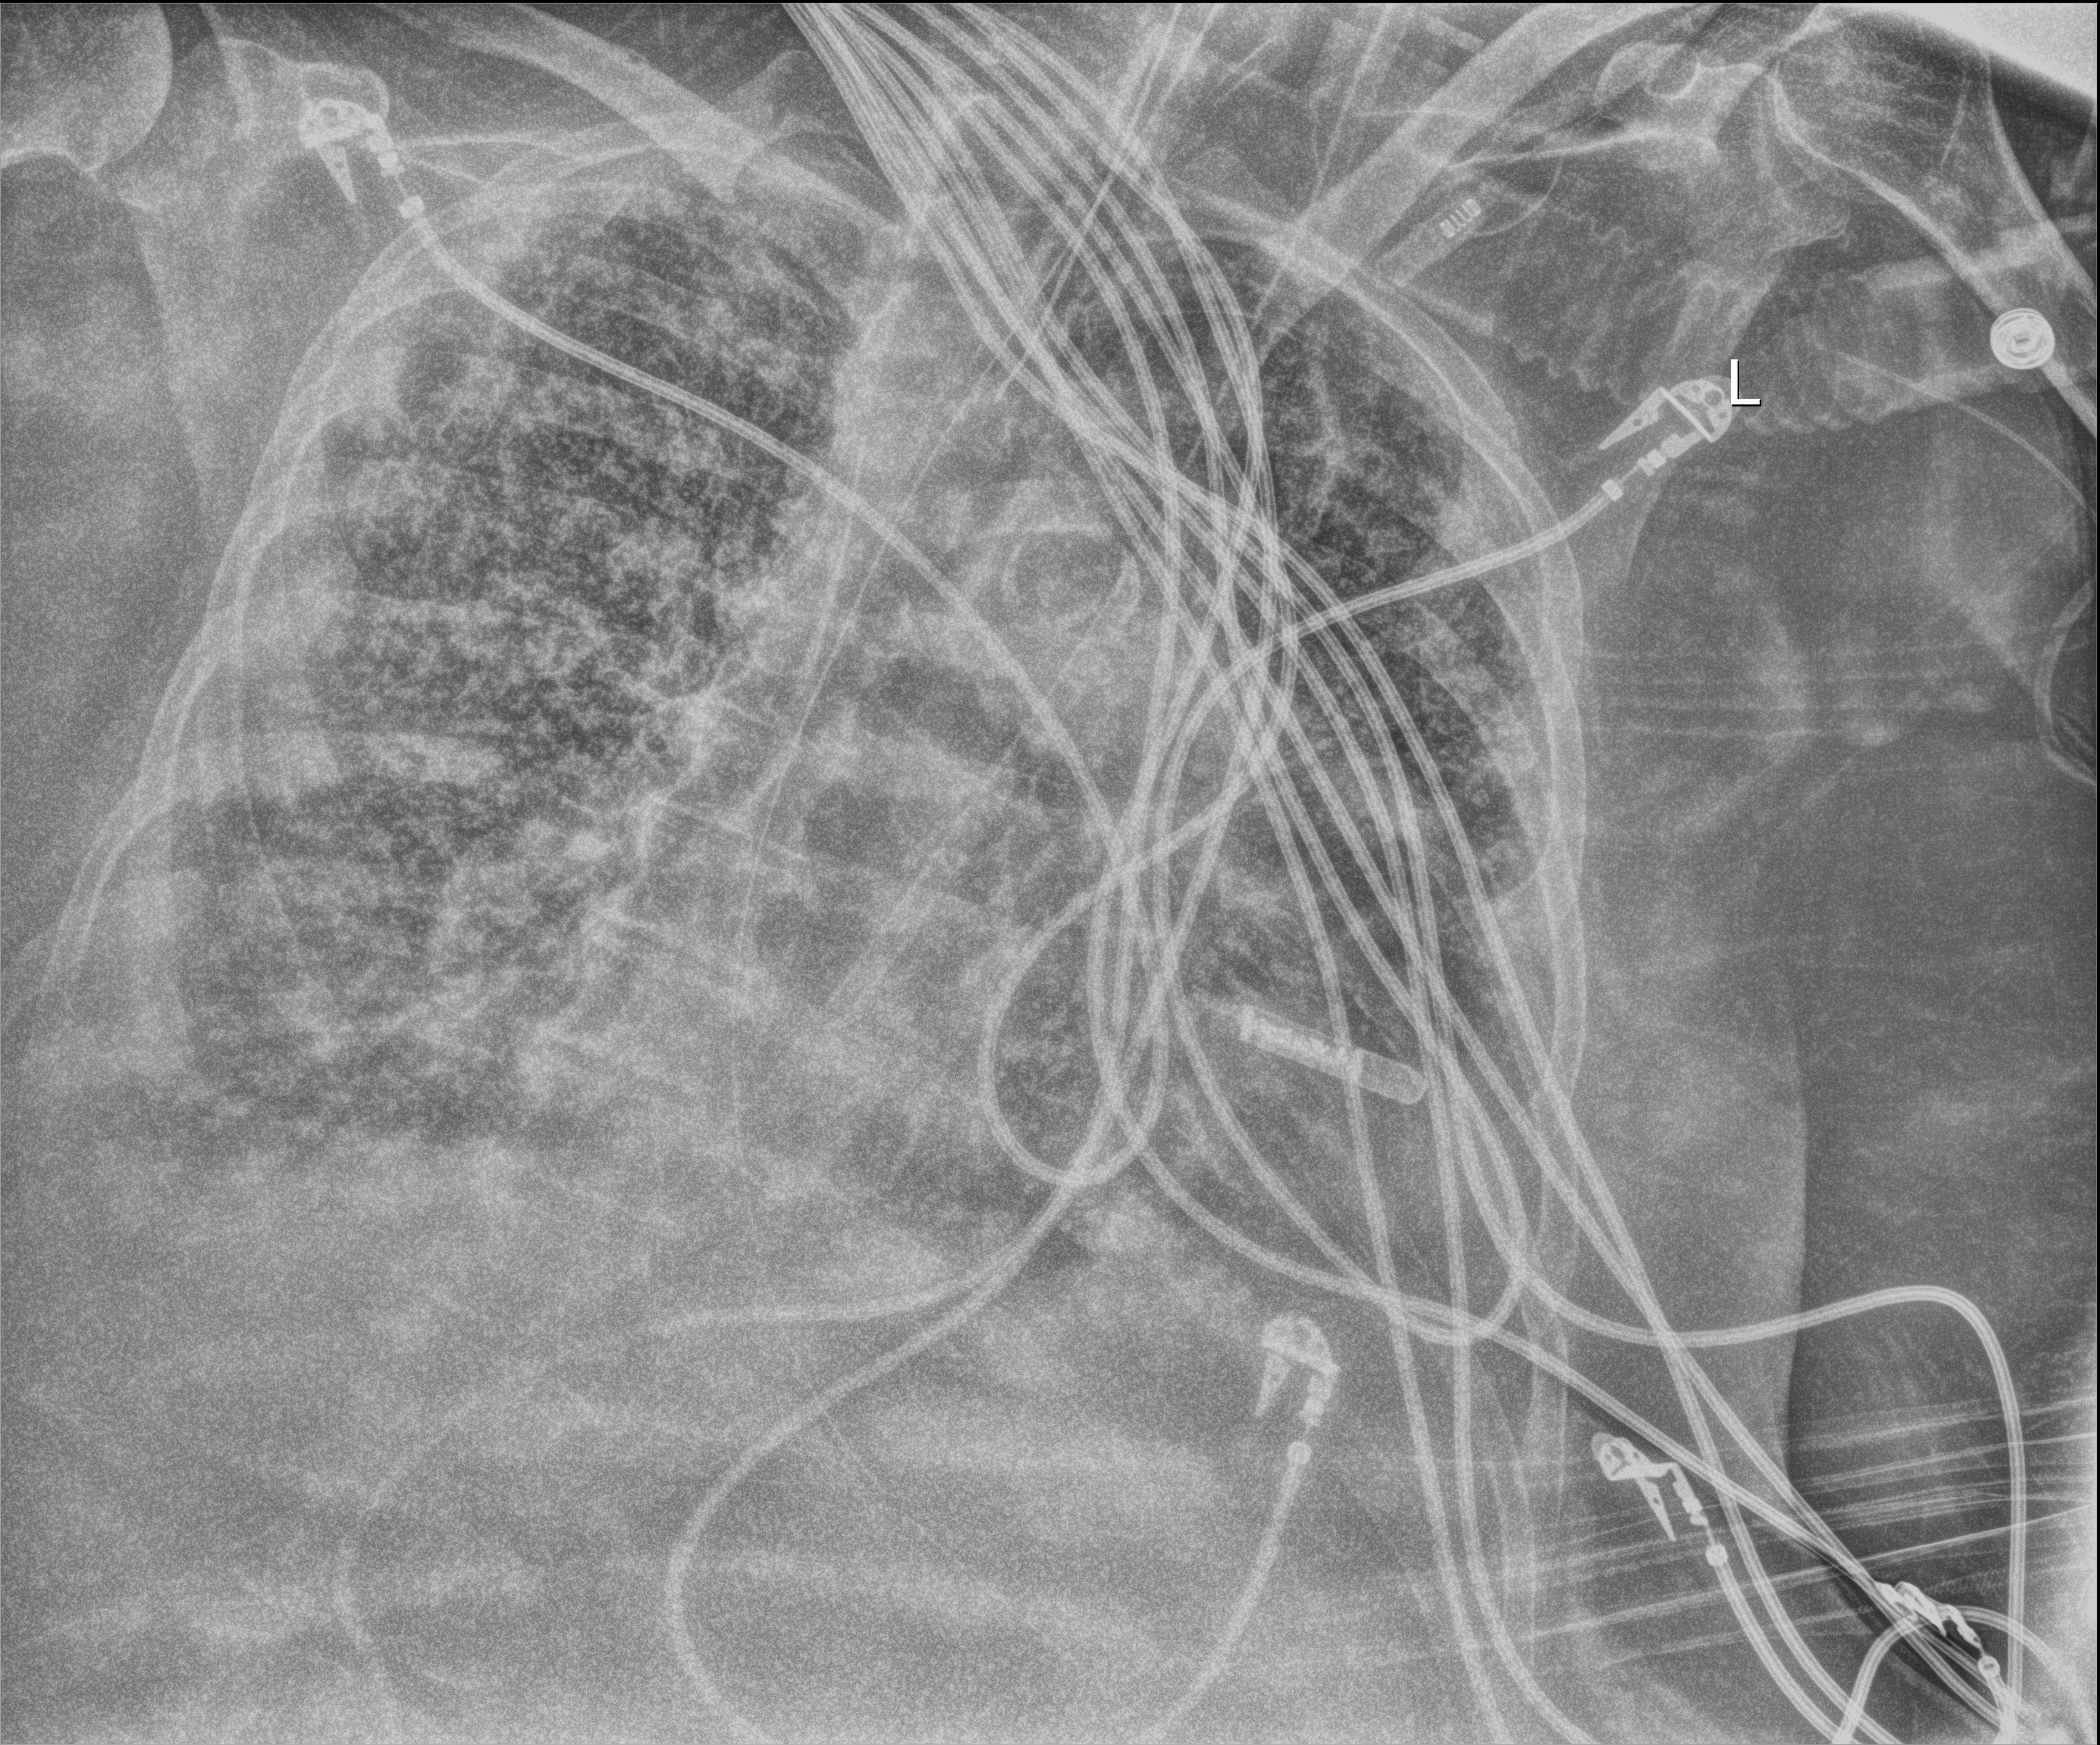
Chest X-ray (portable); anteroposterior (AP) projection. Female patient hospitalised with COVID-19, age 60–74 years.
From the hospital-stay record, not from the radiograph (when in the stay this image was taken is not recorded):
- admitted to intensive care during this hospital stay: yes
- mechanically ventilated during this hospital stay: yes
- smoking status (admission record): former